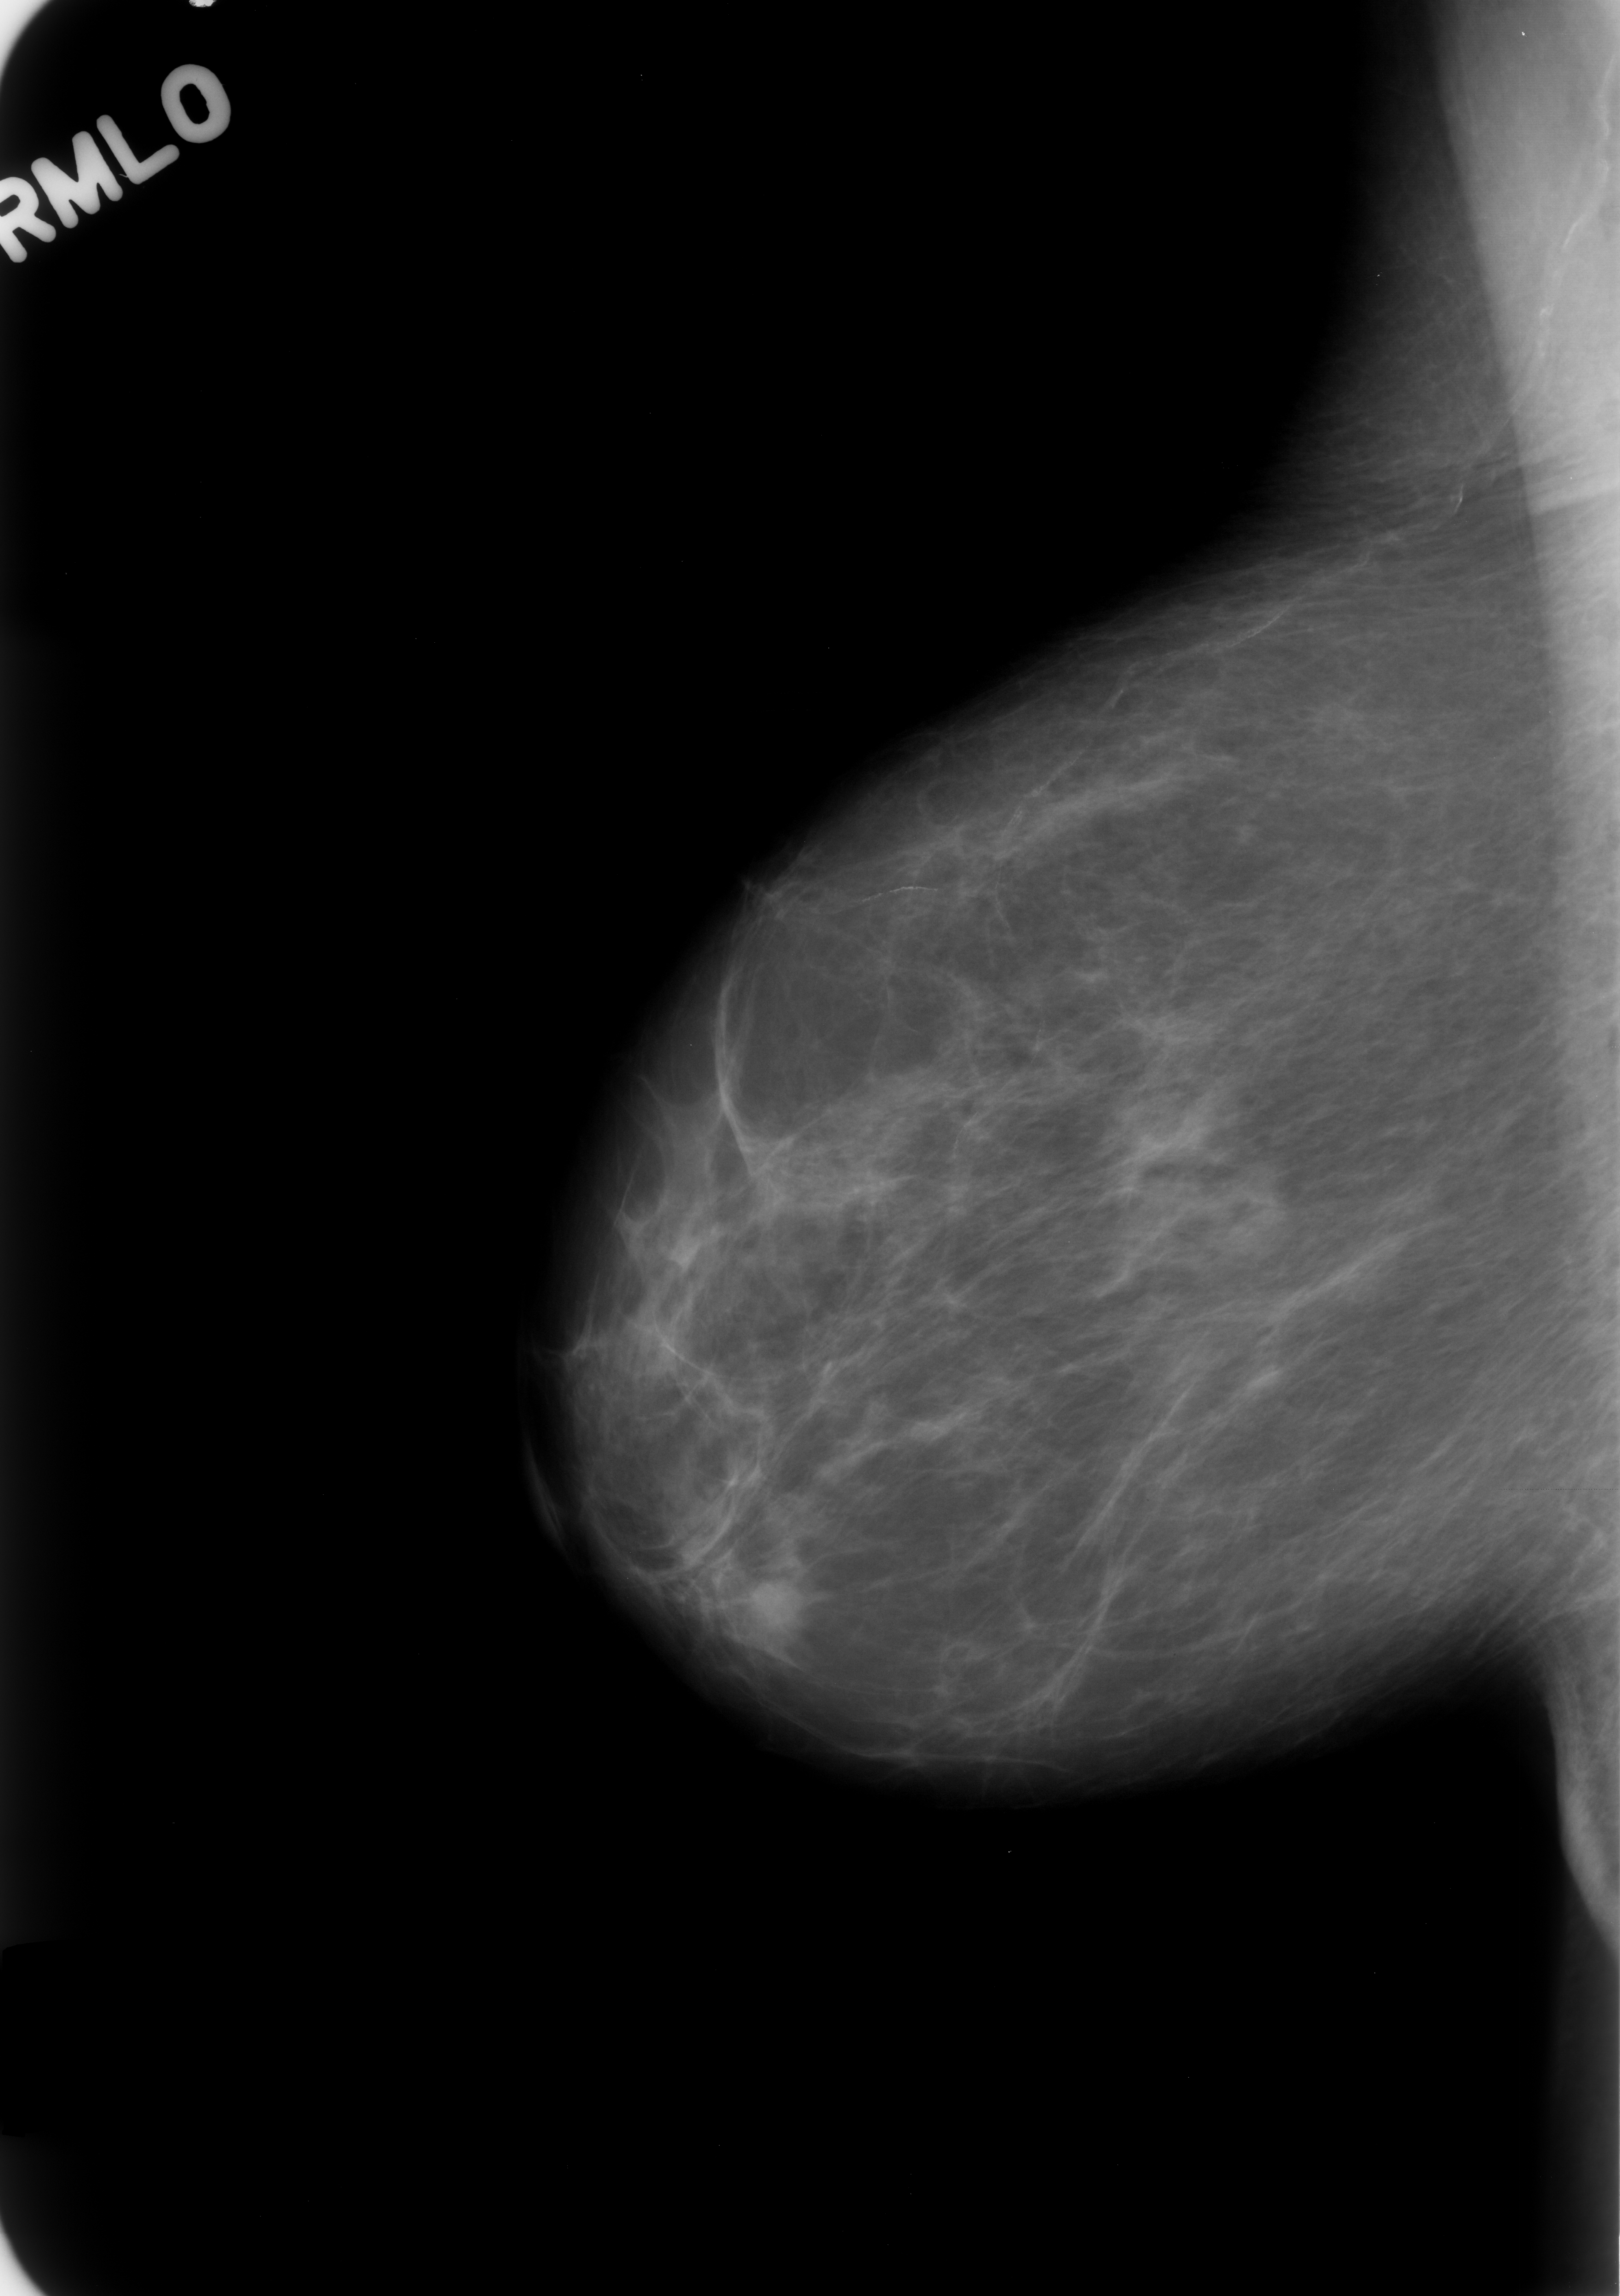
Scanned film-screen mammogram, right breast, MLO view.
Marked findings (only marked abnormalities are described; nothing is implied about the rest of the image): mass, shape round, margins microlobulated; BI-RADS assessment category 3; subtlety rating 5 on a 1 (subtle) to 5 (obvious) scale; benign without callback (not worked up further).